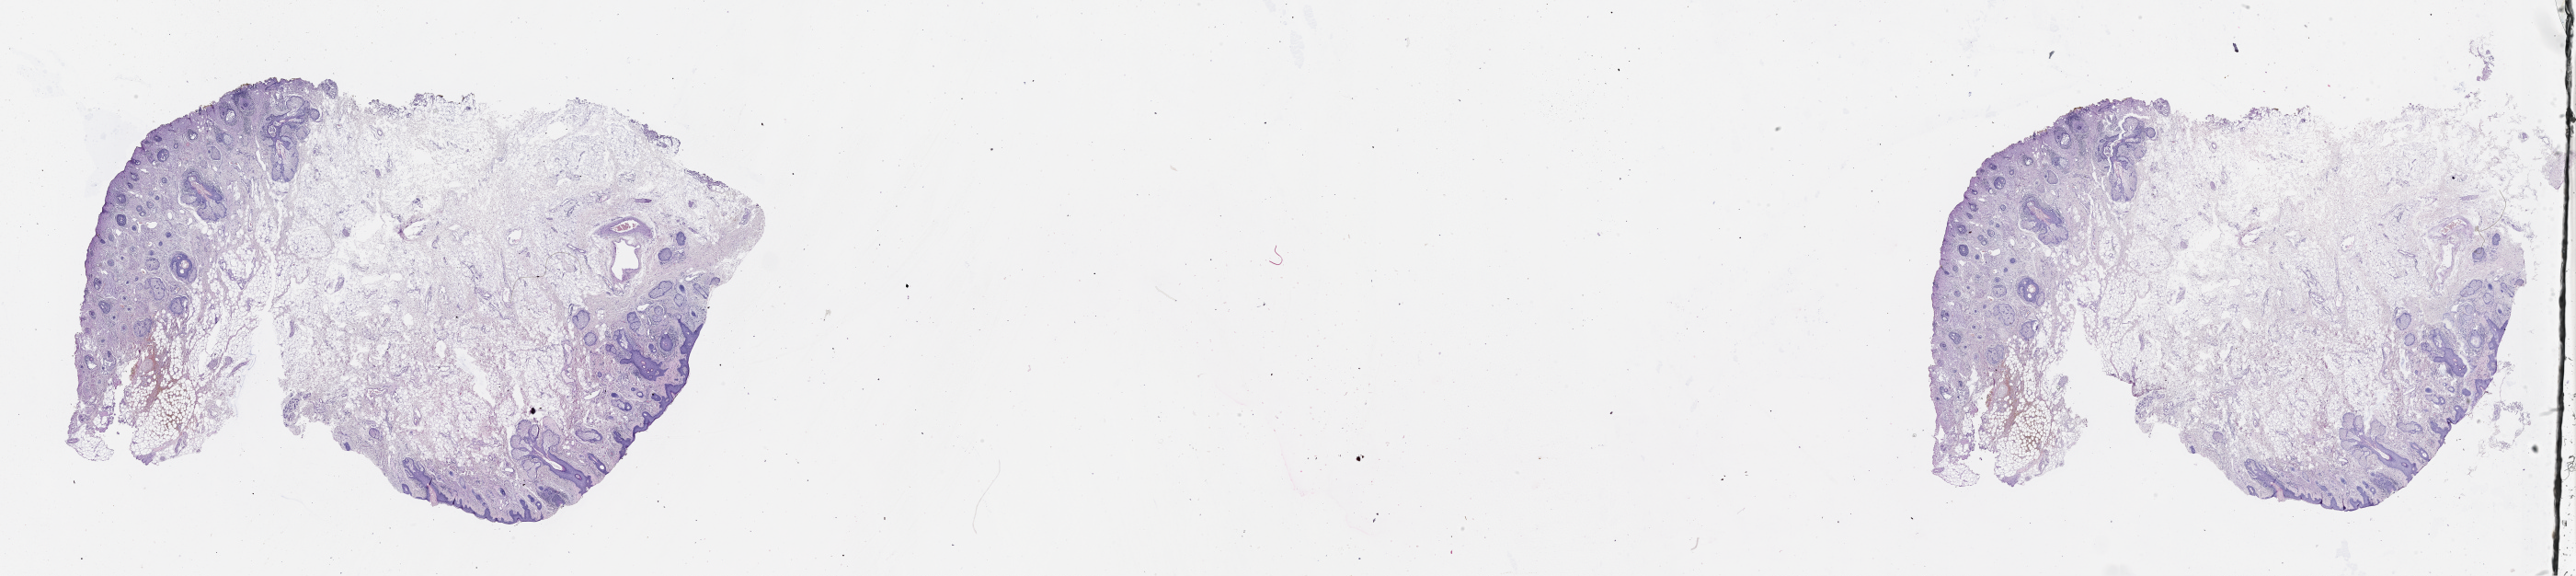
Whole-slide histology image, Hematoxylin and eosin (H&E) stained, whole scanned area (about 45.1 x 10.1 mm) shown as a low-resolution overview; normal (non-tumour) tissue sample, sampled site: head & neck. Patient: male, age 83 years.
This section: normal (non-tumour) tissue from the same patient. Patient diagnosis: Malignant melanoma, NOS.